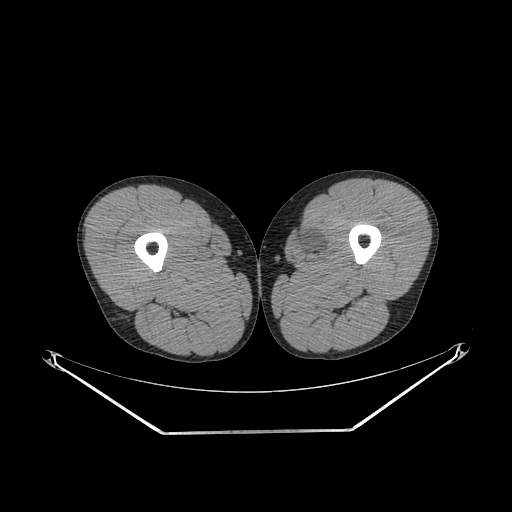
CT of an extremity soft-tissue mass (from a PET/CT study), one axial slice; slice 261 of 311 in the series (ordered by position); soft-tissue window (W 400 / L 40 HU); 512 × 512 image matrix. Male patient. From the clinical record (not read from this slice): histological type: mixoid liposarcoma; grade: low; site of the primary tumour: left thigh.
Structures marked on this image (expert contour drawn on MRI and transferred to this co-registered scan by the dataset authors):
- gross tumour volume (mass): box from (x=297, y=230) to (x=323, y=257) px